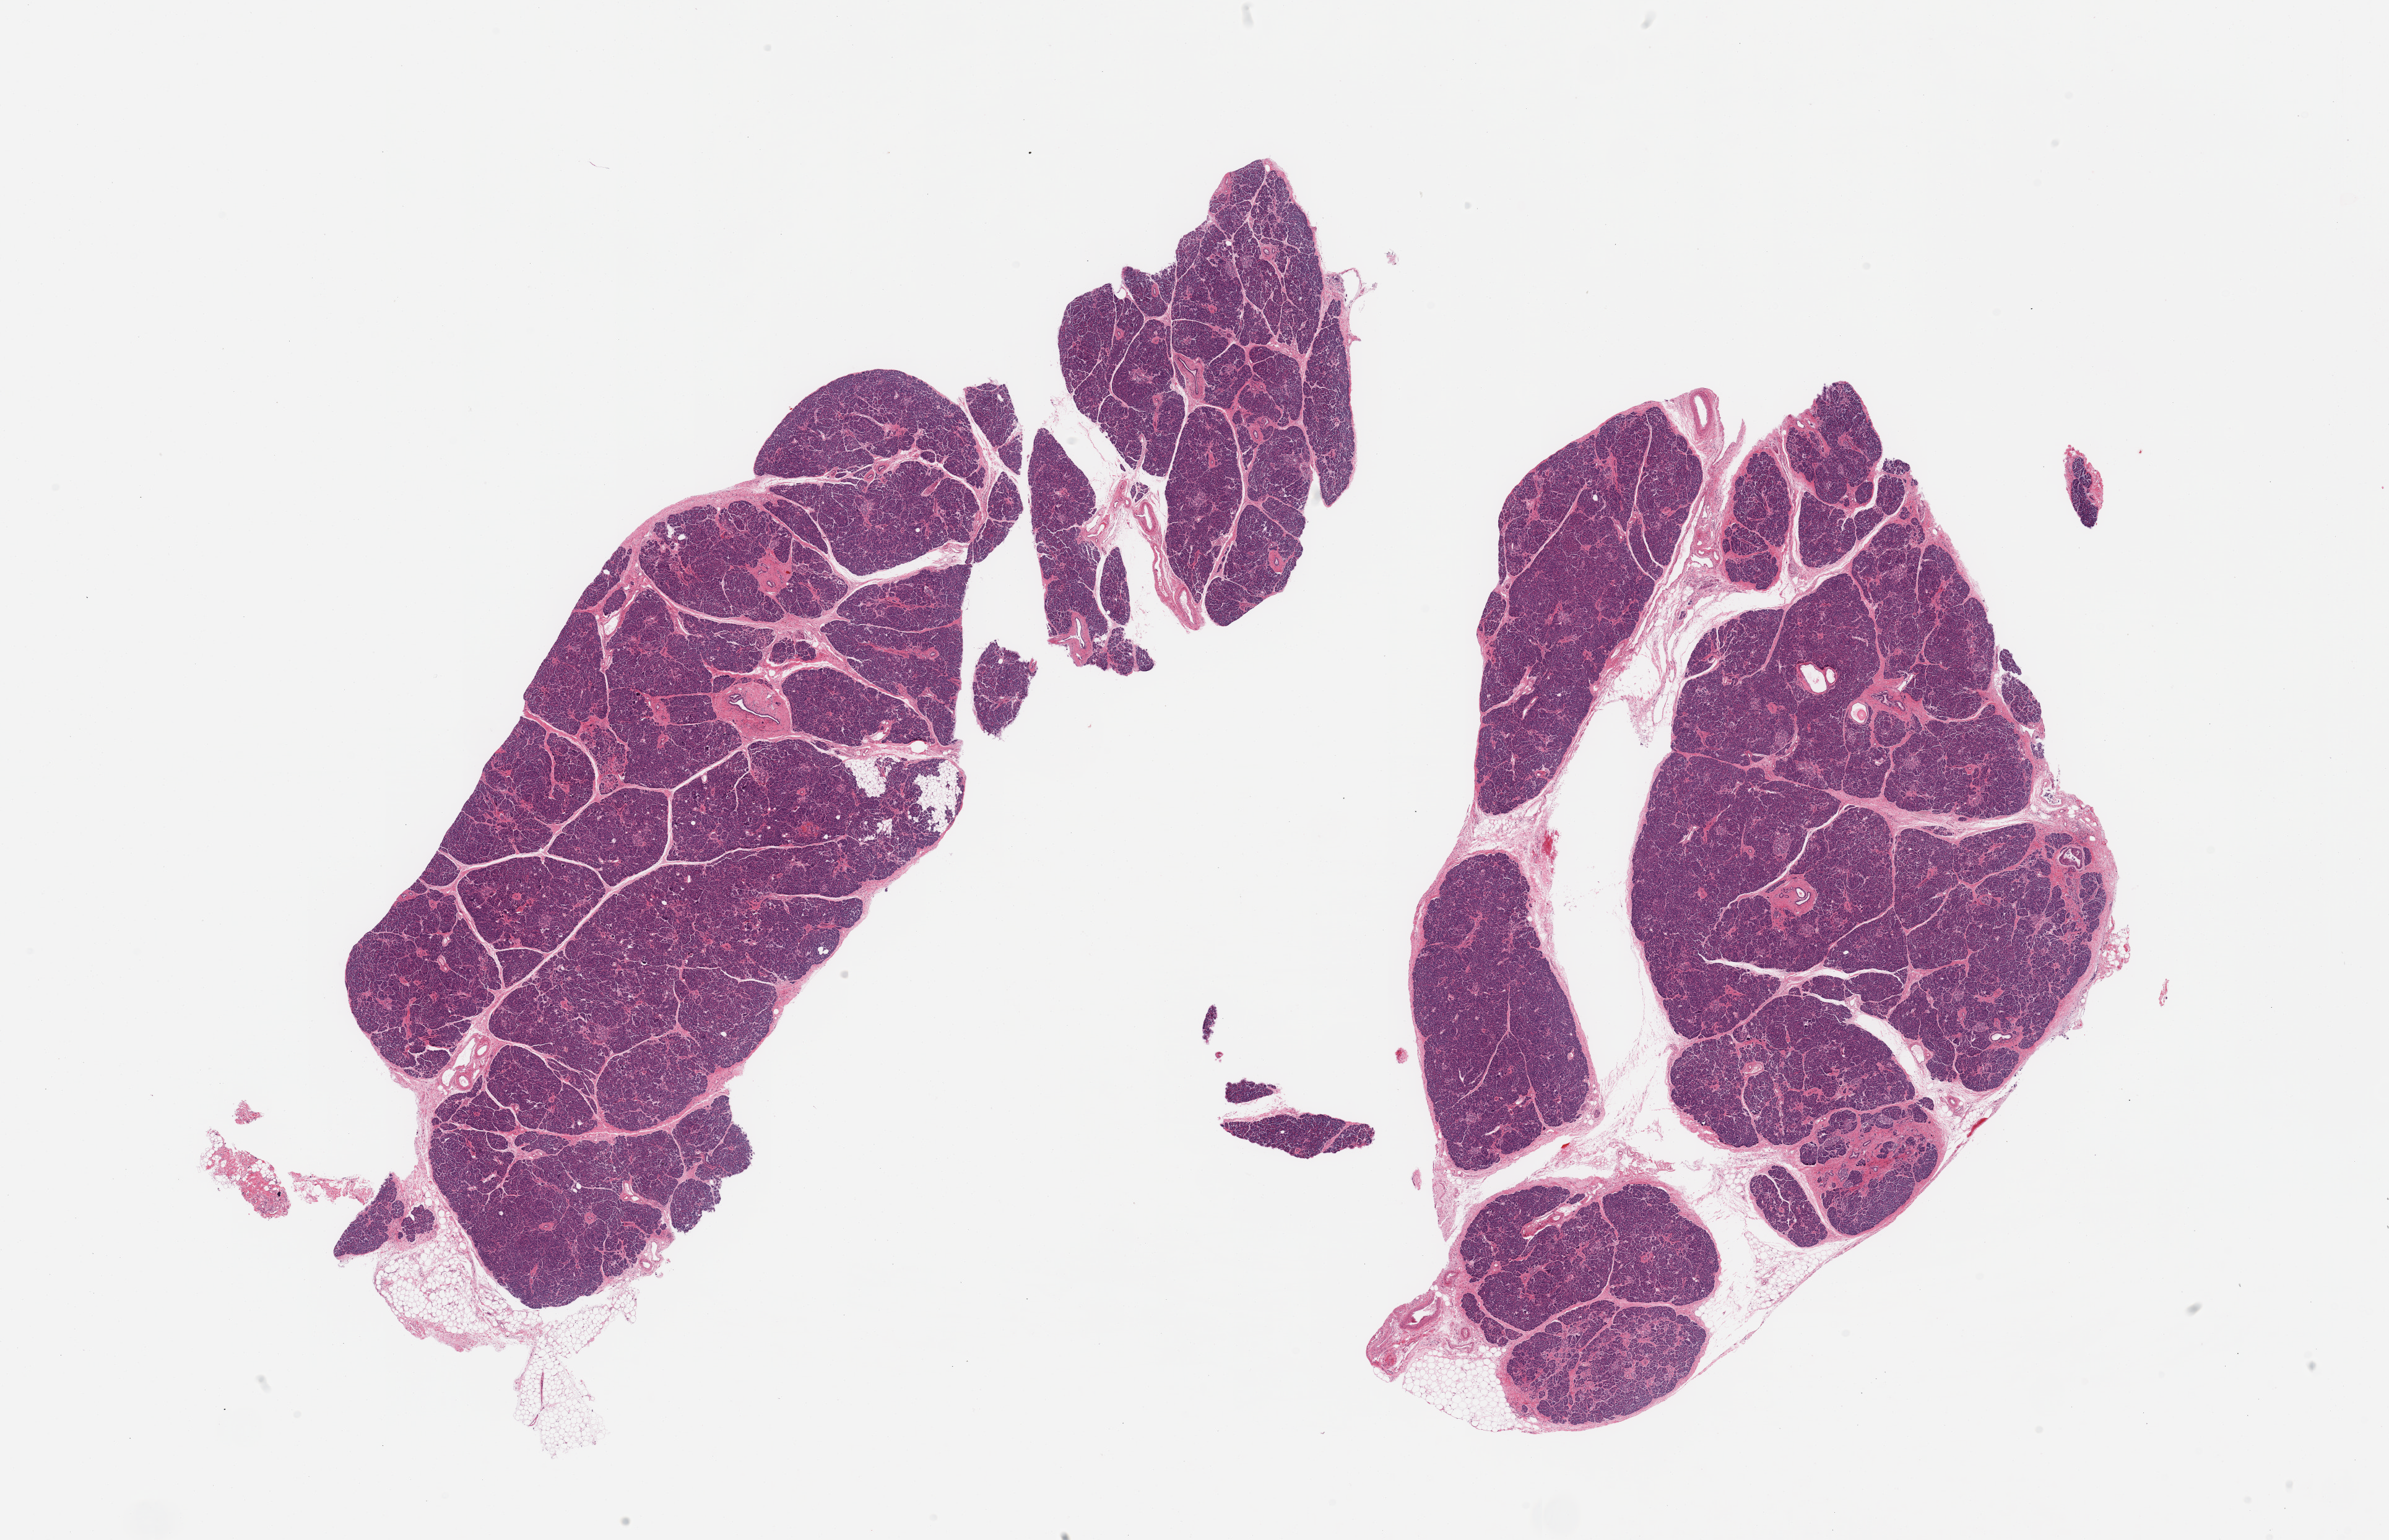
Whole-slide image, haematoxylin and eosin stain — shown as a low-resolution overview of the whole scanned area (about 30.5 x 19.7 mm, slide scanned at 20x). PAXgene-fixed paraffin-embedded (PFPE) section. Section of pancreas (target tissue). Donor tissue sample. Donor: male.
Reviewer comment on this tissue sample: 2 pieces, minimal fat; Islets well-preserved.